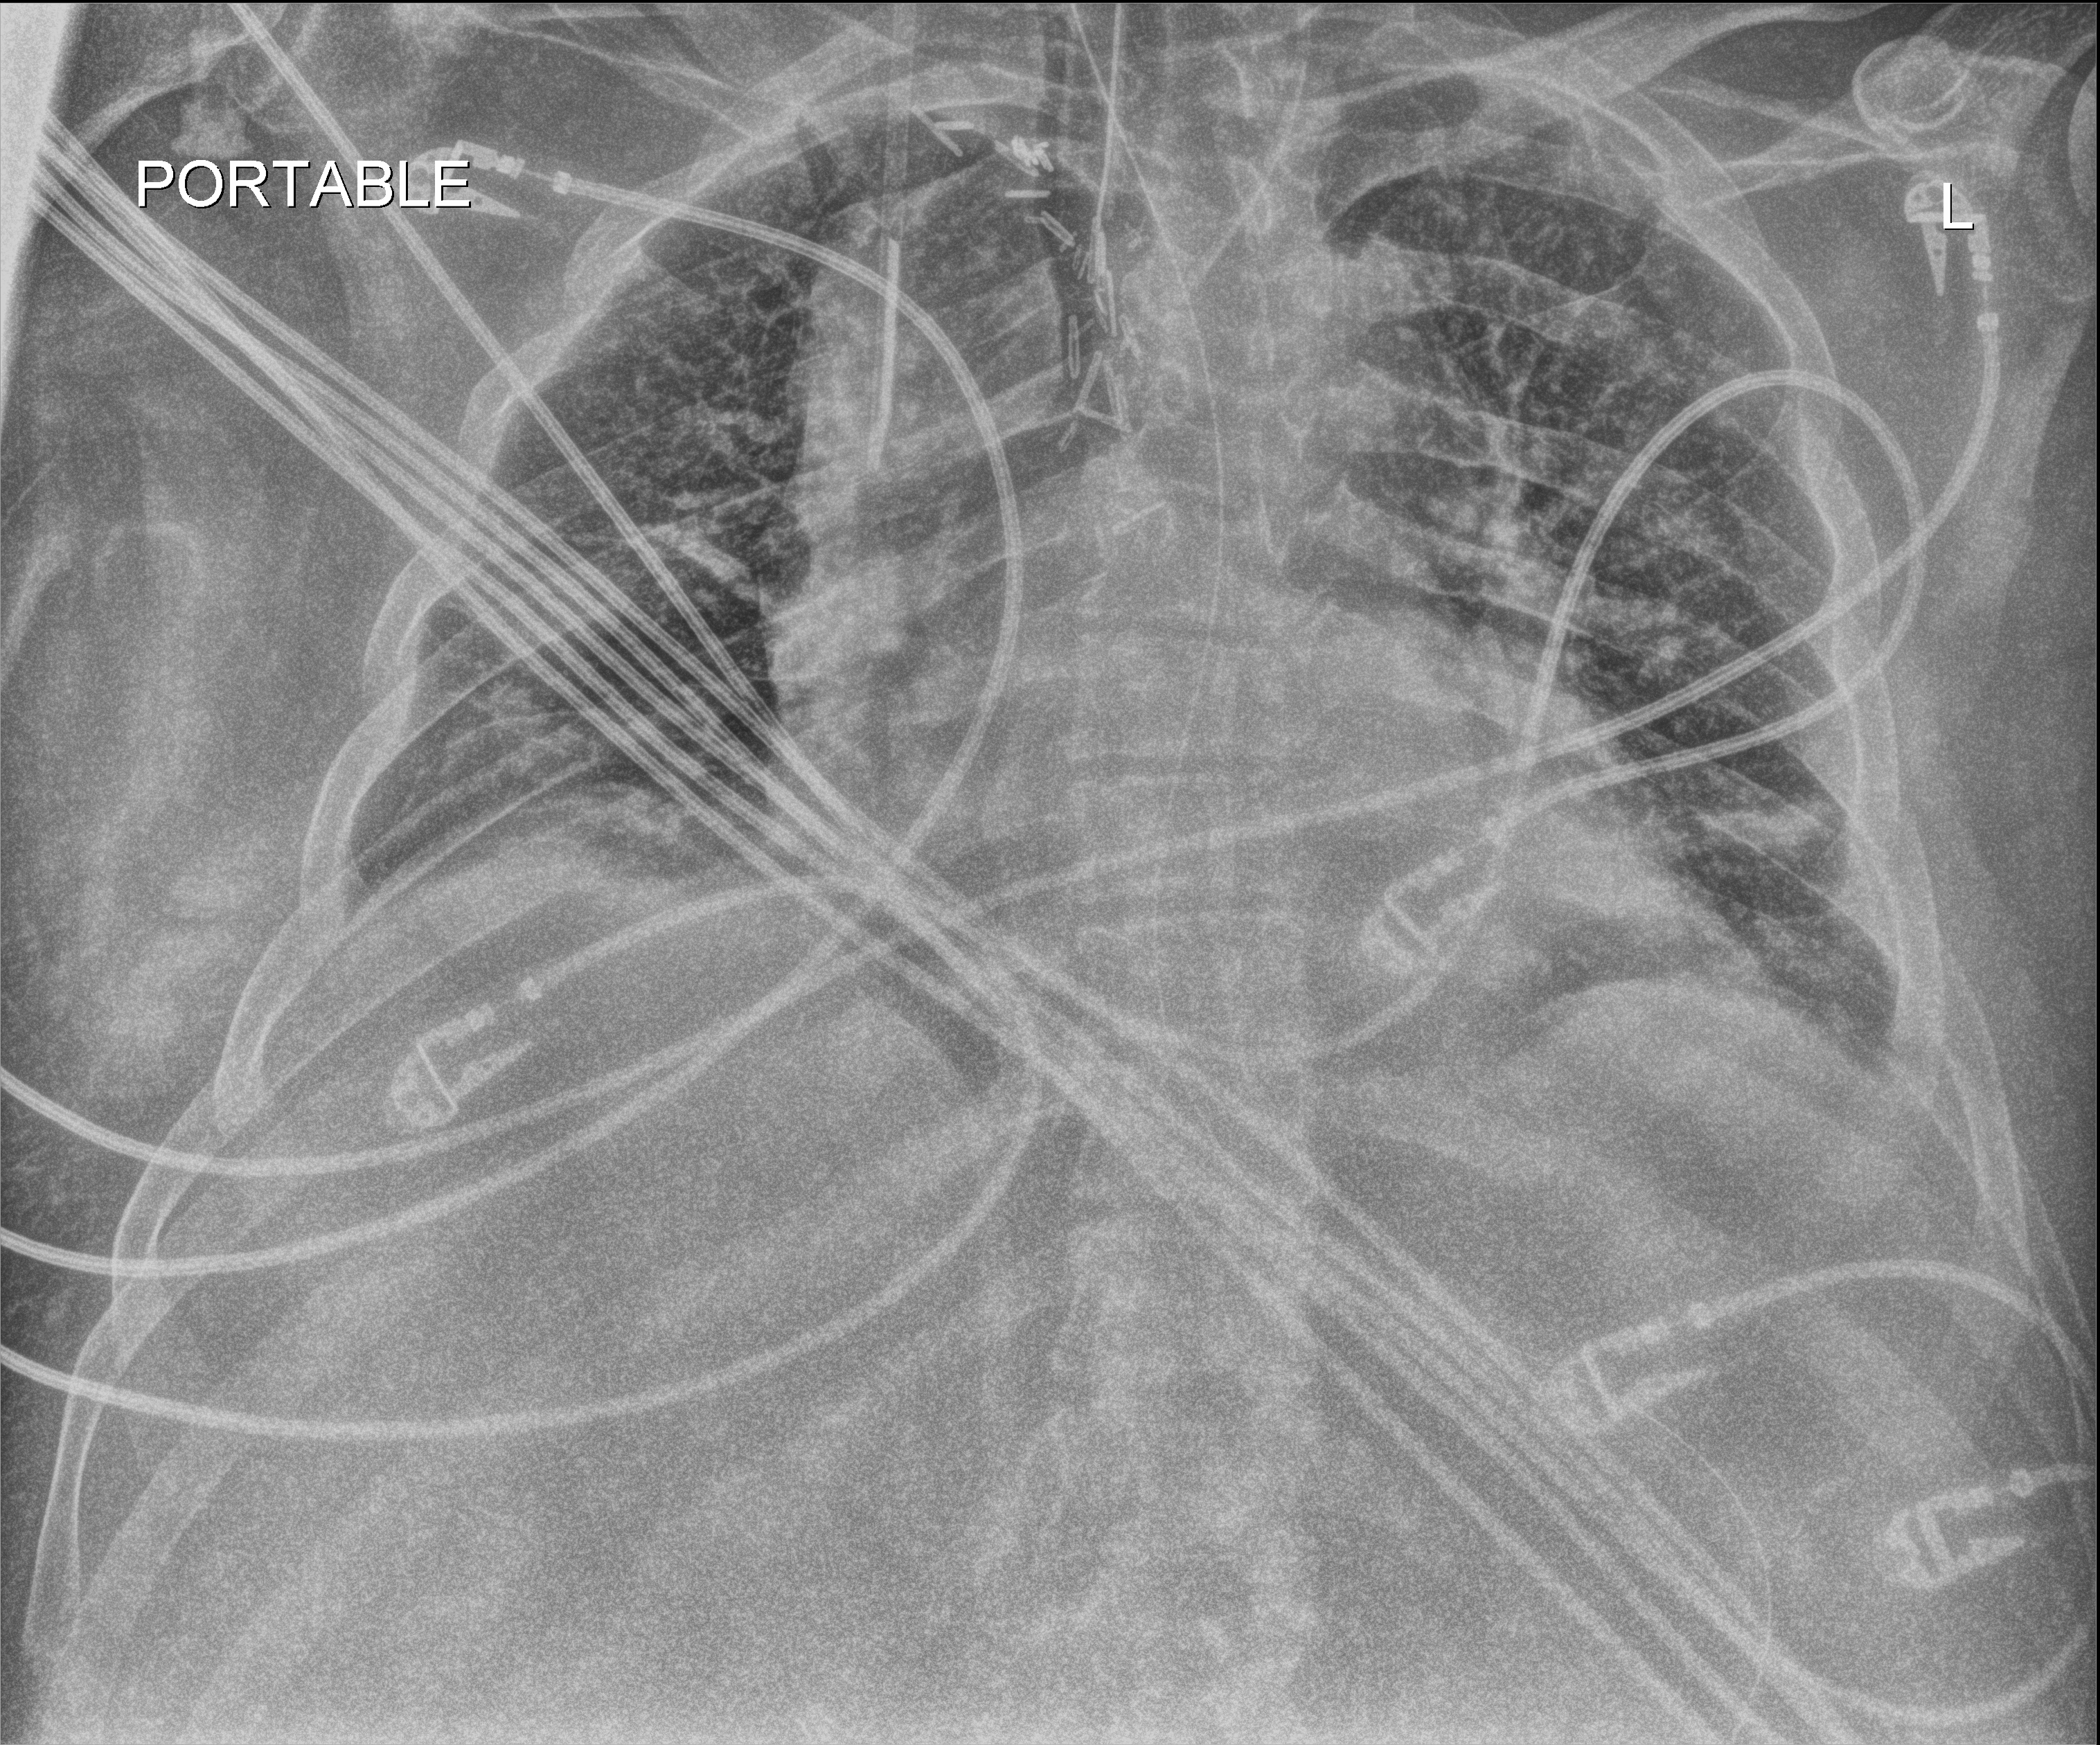
Bedside chest radiograph (digital radiography); anteroposterior (AP) projection. Adult patient hospitalised with COVID-19, age 18–59 years.
Admission-level facts for this patient (not findings on this image; timing relative to this image not recorded):
- length of hospital stay: 2 days
- mechanically ventilated during this hospital stay: yes